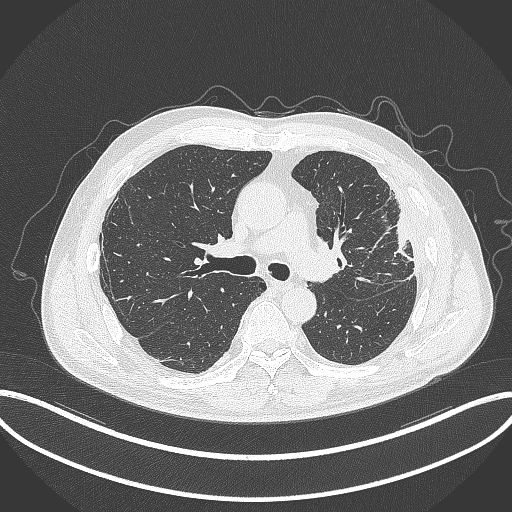
Chest CT, one axial slice. Position 212 of 382 along the scan axis. Reconstruction kernel B70f. 120 kVp. Lung window (W 1500 / L -600 HU). 1 mm slice thickness. 512 × 512 image matrix, field of view 415 × 415 mm. Patient: male, 64 years. Case-level facts recorded for this patient, not image findings: clinical TNM (as recorded): T4 N1 M0.
Annotated regions visible in this slice (rectangle marked by the reading radiologist):
- lung tumour (recorded histology: adenocarcinoma): bounding box <388,206,415,262> (left, top, right, bottom; pixels)